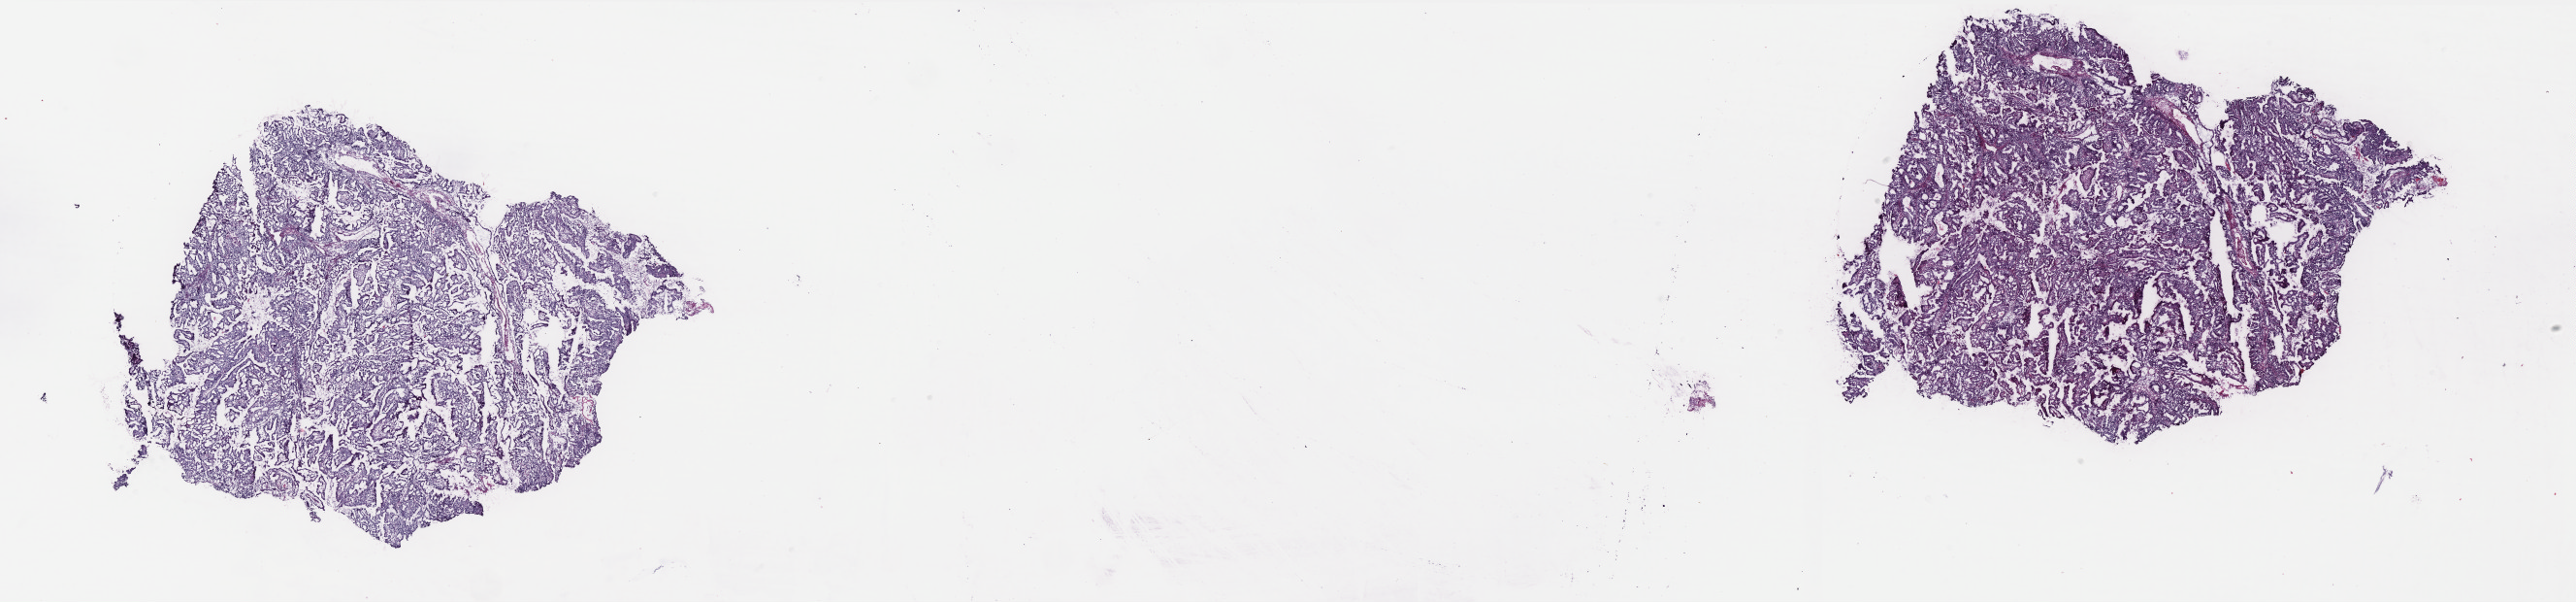
Digitized Hematoxylin and eosin (H&E) stained tissue section (whole slide), shown as a low-resolution overview of the whole scanned area (about 42.6 x 9.9 mm, acquisition: 40x scan). Frozen section from the bottom of the tissue portion. Primary tumour sample from the uterus. Female patient; age at initial diagnosis 73 years. Histologic grade: G2 (moderately differentiated). Pathologist review of this section (percent, as recorded): tumour cells 100%, tumour nuclei 90%, normal cells 0%, stromal cells 0%, necrosis 0%. Inflammatory infiltration, as recorded: lymphocyte infiltration 0%, monocyte infiltration 0%, neutrophil infiltration 0%.
* diagnosis: Endometrioid adenocarcinoma, NOS (endometrium)
* FIGO stage: IB